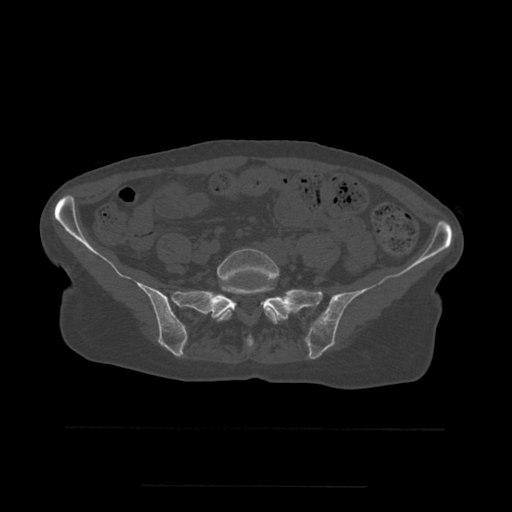
CT including the spine, one axial slice. Bone window (W 1800 / L 400 HU). 512 × 512 image matrix, field of view 350 × 350 mm. Patient age 58 years. From the clinical record (not read from this slice): primary cancer: lung.
Annotated regions visible in this slice (semi-automatic segmentation, software-assisted and operator-edited):
- L5 vertebra: box from (x=217, y=249) to (x=279, y=324) px